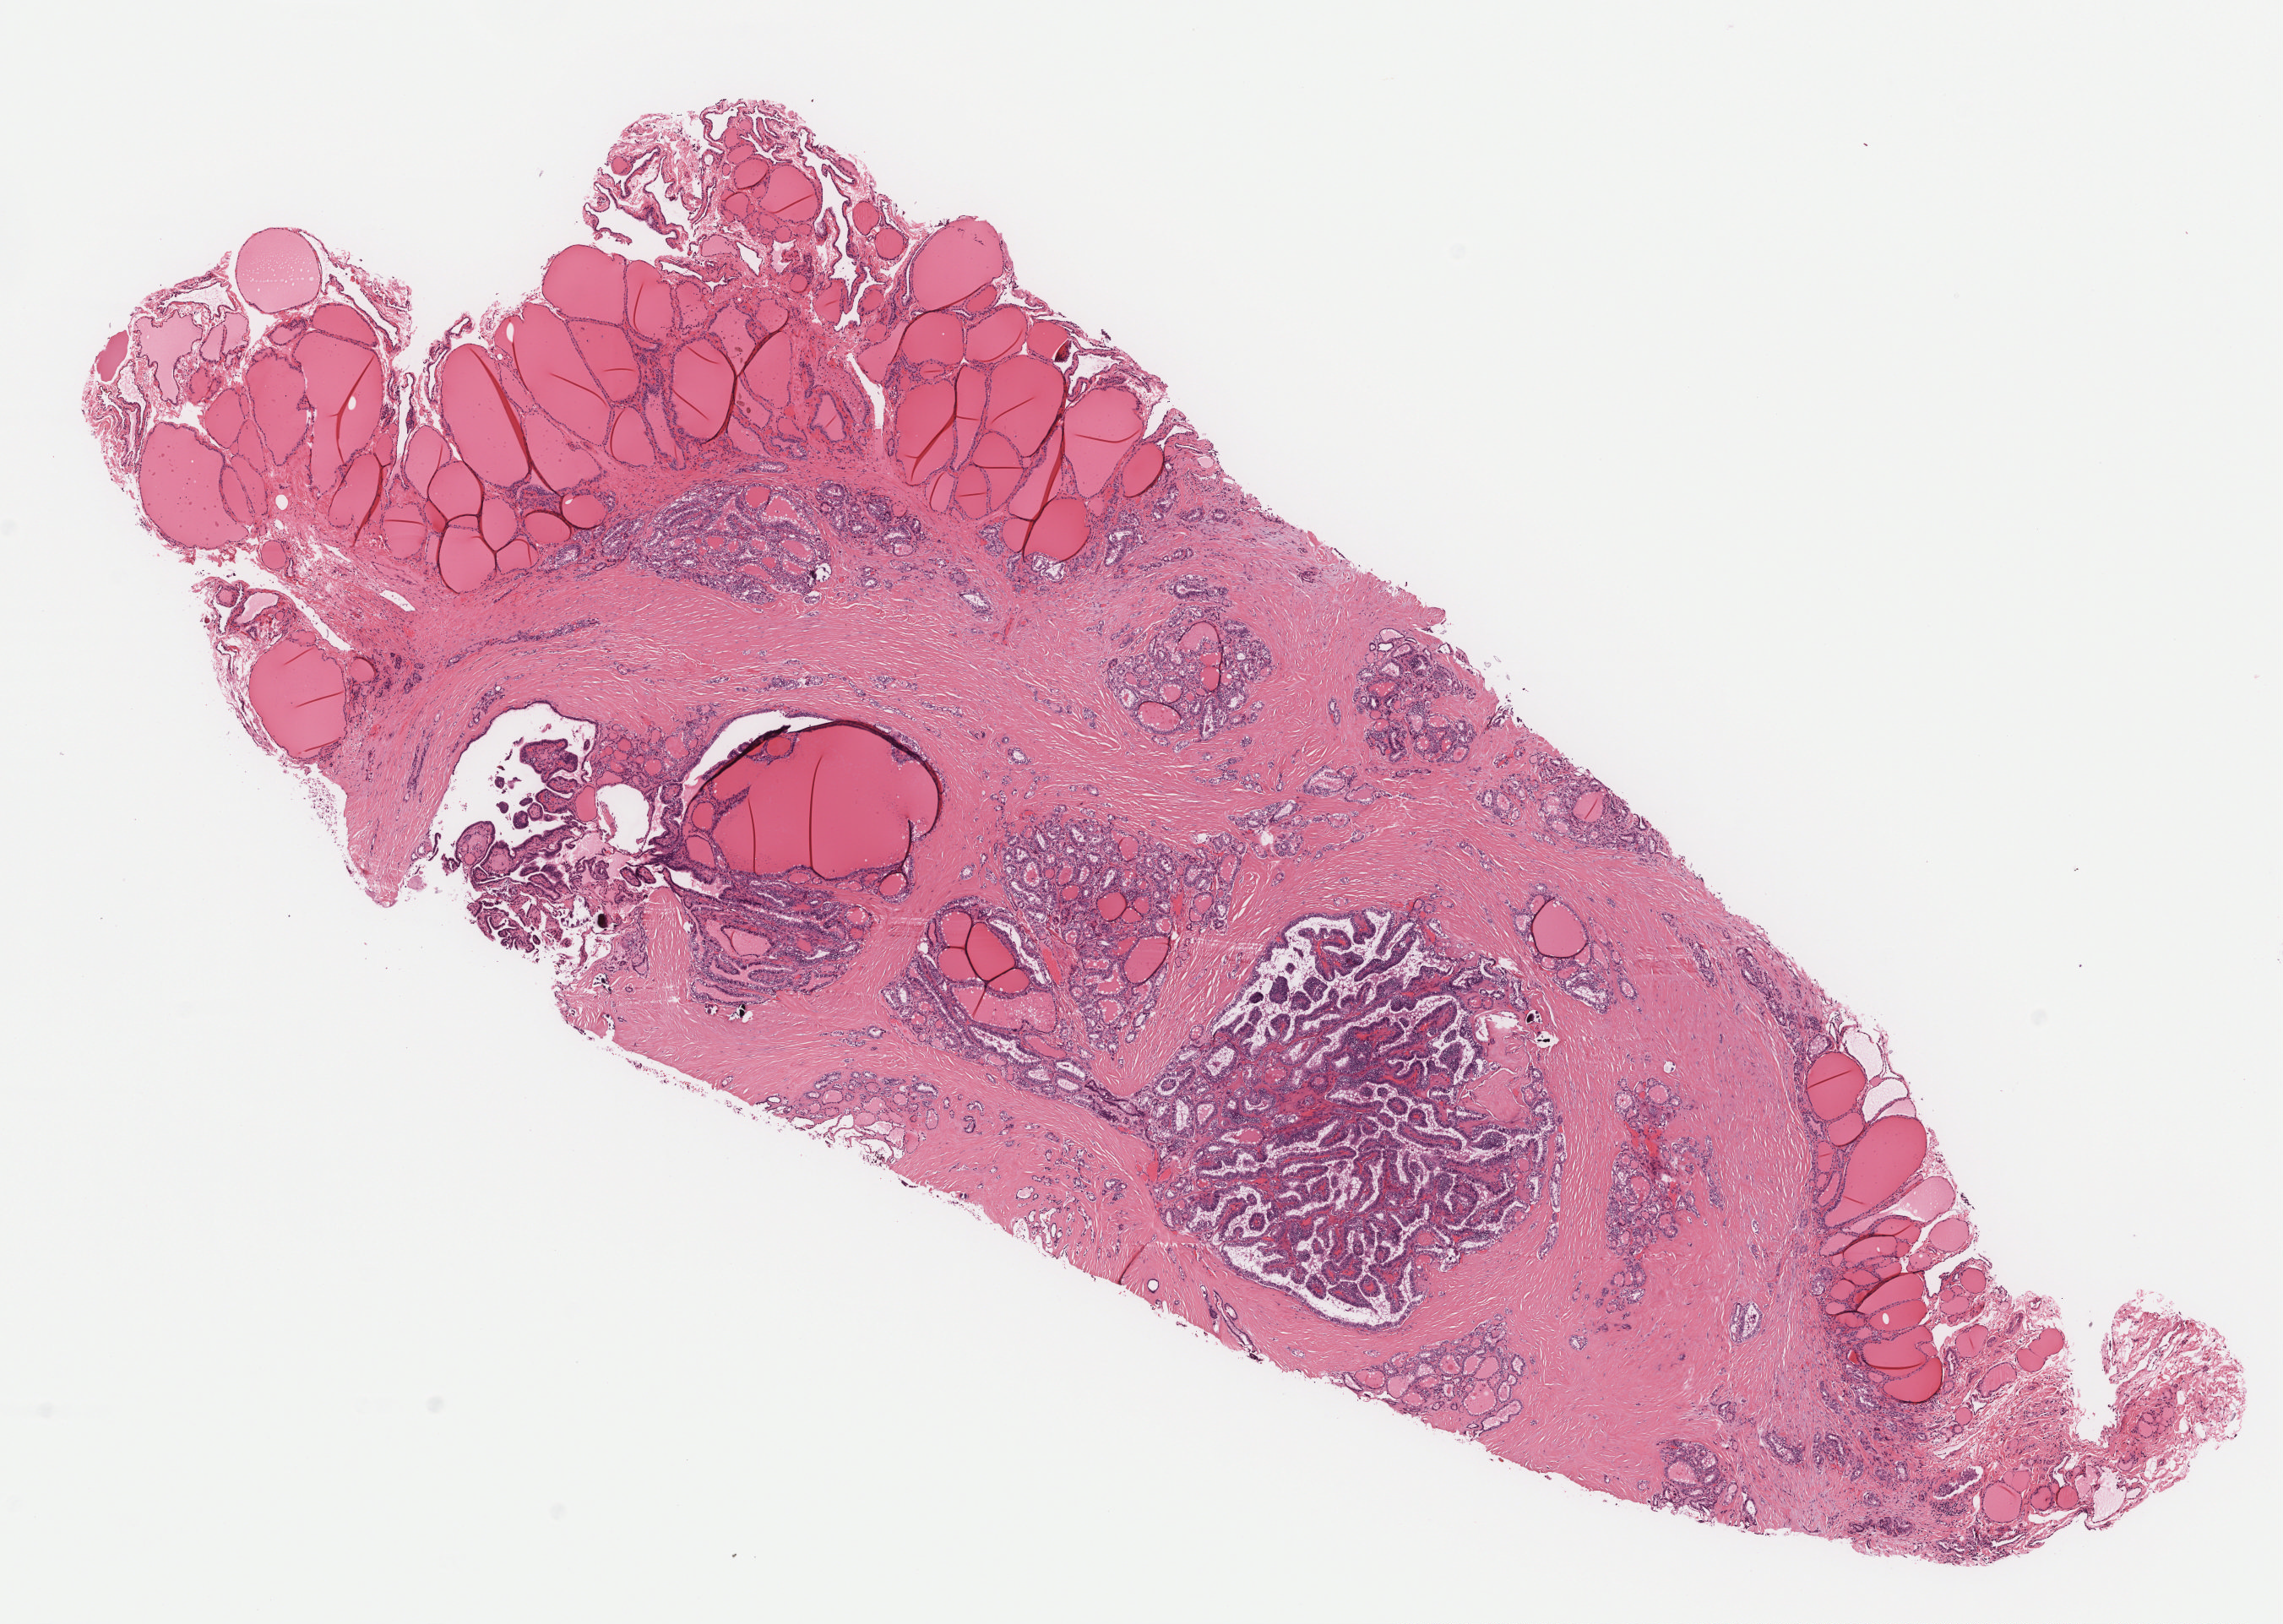
Whole-slide histology image, H&E-stained — whole scanned area (about 10.9 x 7.7 mm, from a 40x scan) shown as a low-resolution overview. Formalin-fixed paraffin-embedded (FFPE) diagnostic section. Primary tumour sample from the thyroid. Male, age 41 years at initial diagnosis.
AJCC pathologic stage: I. Pathologic diagnosis: Papillary adenocarcinoma, NOS. Lymph nodes positive (case pathology): 1 of 1 examined.